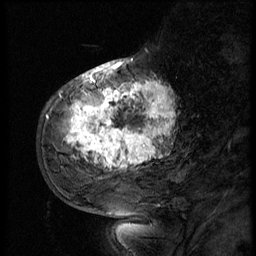
Breast MRI (dynamic contrast-enhanced), one sagittal slice. Slice 19 of 56 in the series (ordered by position). 3 images stored at this slice position (order not interpretable as contrast timing). 1.5 T. TE 4.2 ms, TR 9 ms. 2.5 mm slice thickness. 256 × 256 image matrix, field of view 180 × 180 mm. Female patient, age 51 years. From the clinical record (not read from this slice): setting: breast cancer imaged before/during neoadjuvant chemotherapy; receptor status: triple-negative.
Annotated regions visible in this slice (semi-automatically segmented with operator editing):
- analysis volume of interest (the breast-tissue region the enhancement analysis was run in; not a lesion): bounding box (x1, y1, x2, y2) in pixels: (52, 66, 183, 179)
- tumour enhancement mask (voxels above the 140 % enhancement threshold inside the analysis volume of interest): (65, 66, 173, 171)